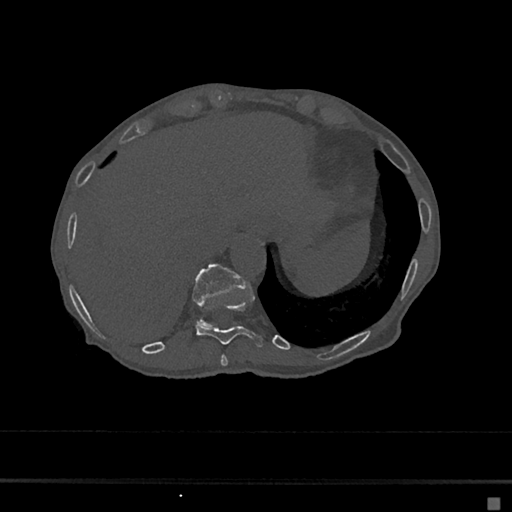
CT including the spine, one axial slice; slice 213 of 797 in the series (ordered by position); bone window (W 1800 / L 400 HU); 512 × 512 image matrix, field of view 360 × 360 mm. Patient: female, 68 years. Case-level facts recorded for this patient, not image findings: primary cancer: renal.
Annotated regions visible in this slice (semi-automatically segmented with operator editing):
- T10 vertebra: box from (x=196, y=300) to (x=264, y=347) px
- T11 vertebra: (x=192, y=263)–(x=247, y=326)
- T9 vertebra: (x=220, y=354)–(x=228, y=366)